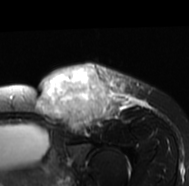
MRI of an extremity soft-tissue mass, one axial slice. Slice 52 of 77 in the series (ordered by position). T2-weighted fat-saturated. MR volume resampled by the dataset authors to the PET/CT grid (not the native acquisition matrix). 3.27 mm slice thickness. 189 × 186 image matrix, field of view 185 × 182 mm. Female patient. Case-level facts recorded for this patient, not image findings: histological type: leiomyosarcoma; grade: high; site of the primary tumour: groin.
Structures marked on this image (expert contour drawn on MRI and transferred to this co-registered scan by the dataset authors):
- gross tumour volume including surrounding oedema: box from (x=35, y=63) to (x=148, y=137) px
- gross tumour volume (mass): (x=35, y=65)–(x=112, y=130)